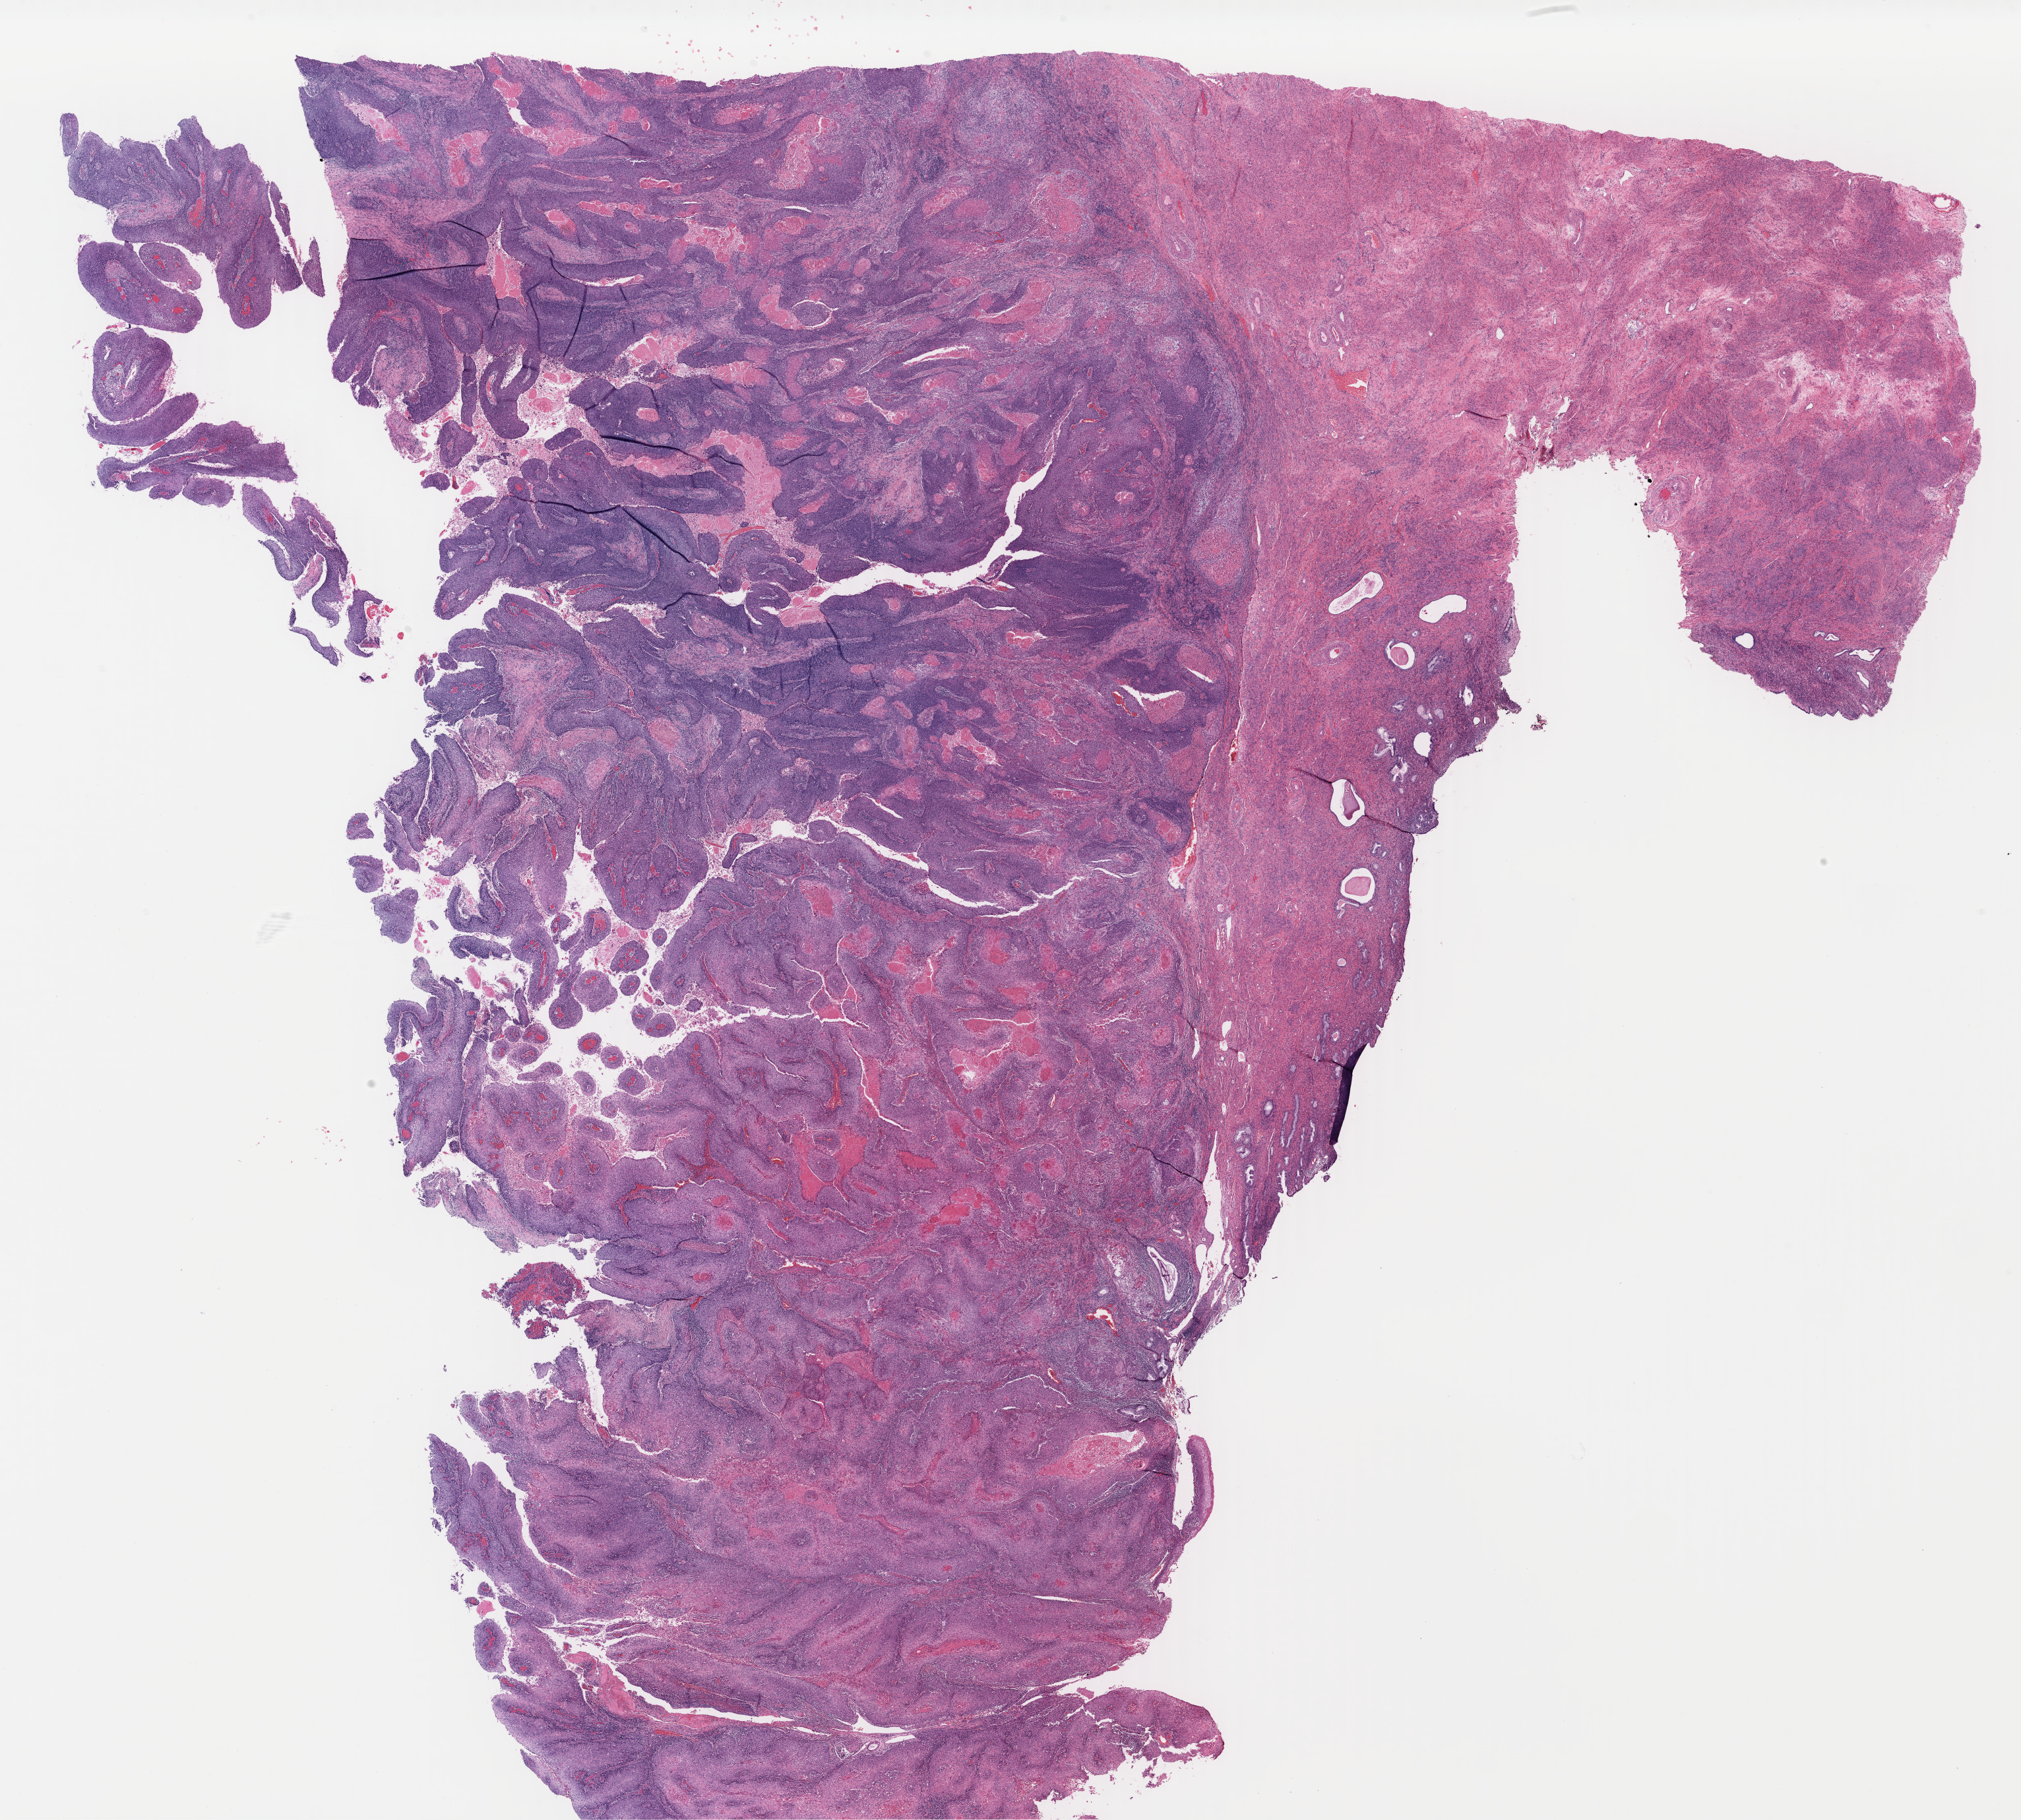
Whole-slide histology image, Hematoxylin and eosin (H&E) stained, shown as a low-resolution overview of the whole scanned area (about 24.1 x 21.7 mm), formalin-fixed paraffin-embedded (FFPE) diagnostic section, primary tumour sample from the cervix. Female, age 68 years at initial diagnosis. Histologic grade: G1 (well differentiated).
Pathologic diagnosis: Squamous cell carcinoma, keratinizing, NOS (cervix uteri). FIGO stage: IIA2.